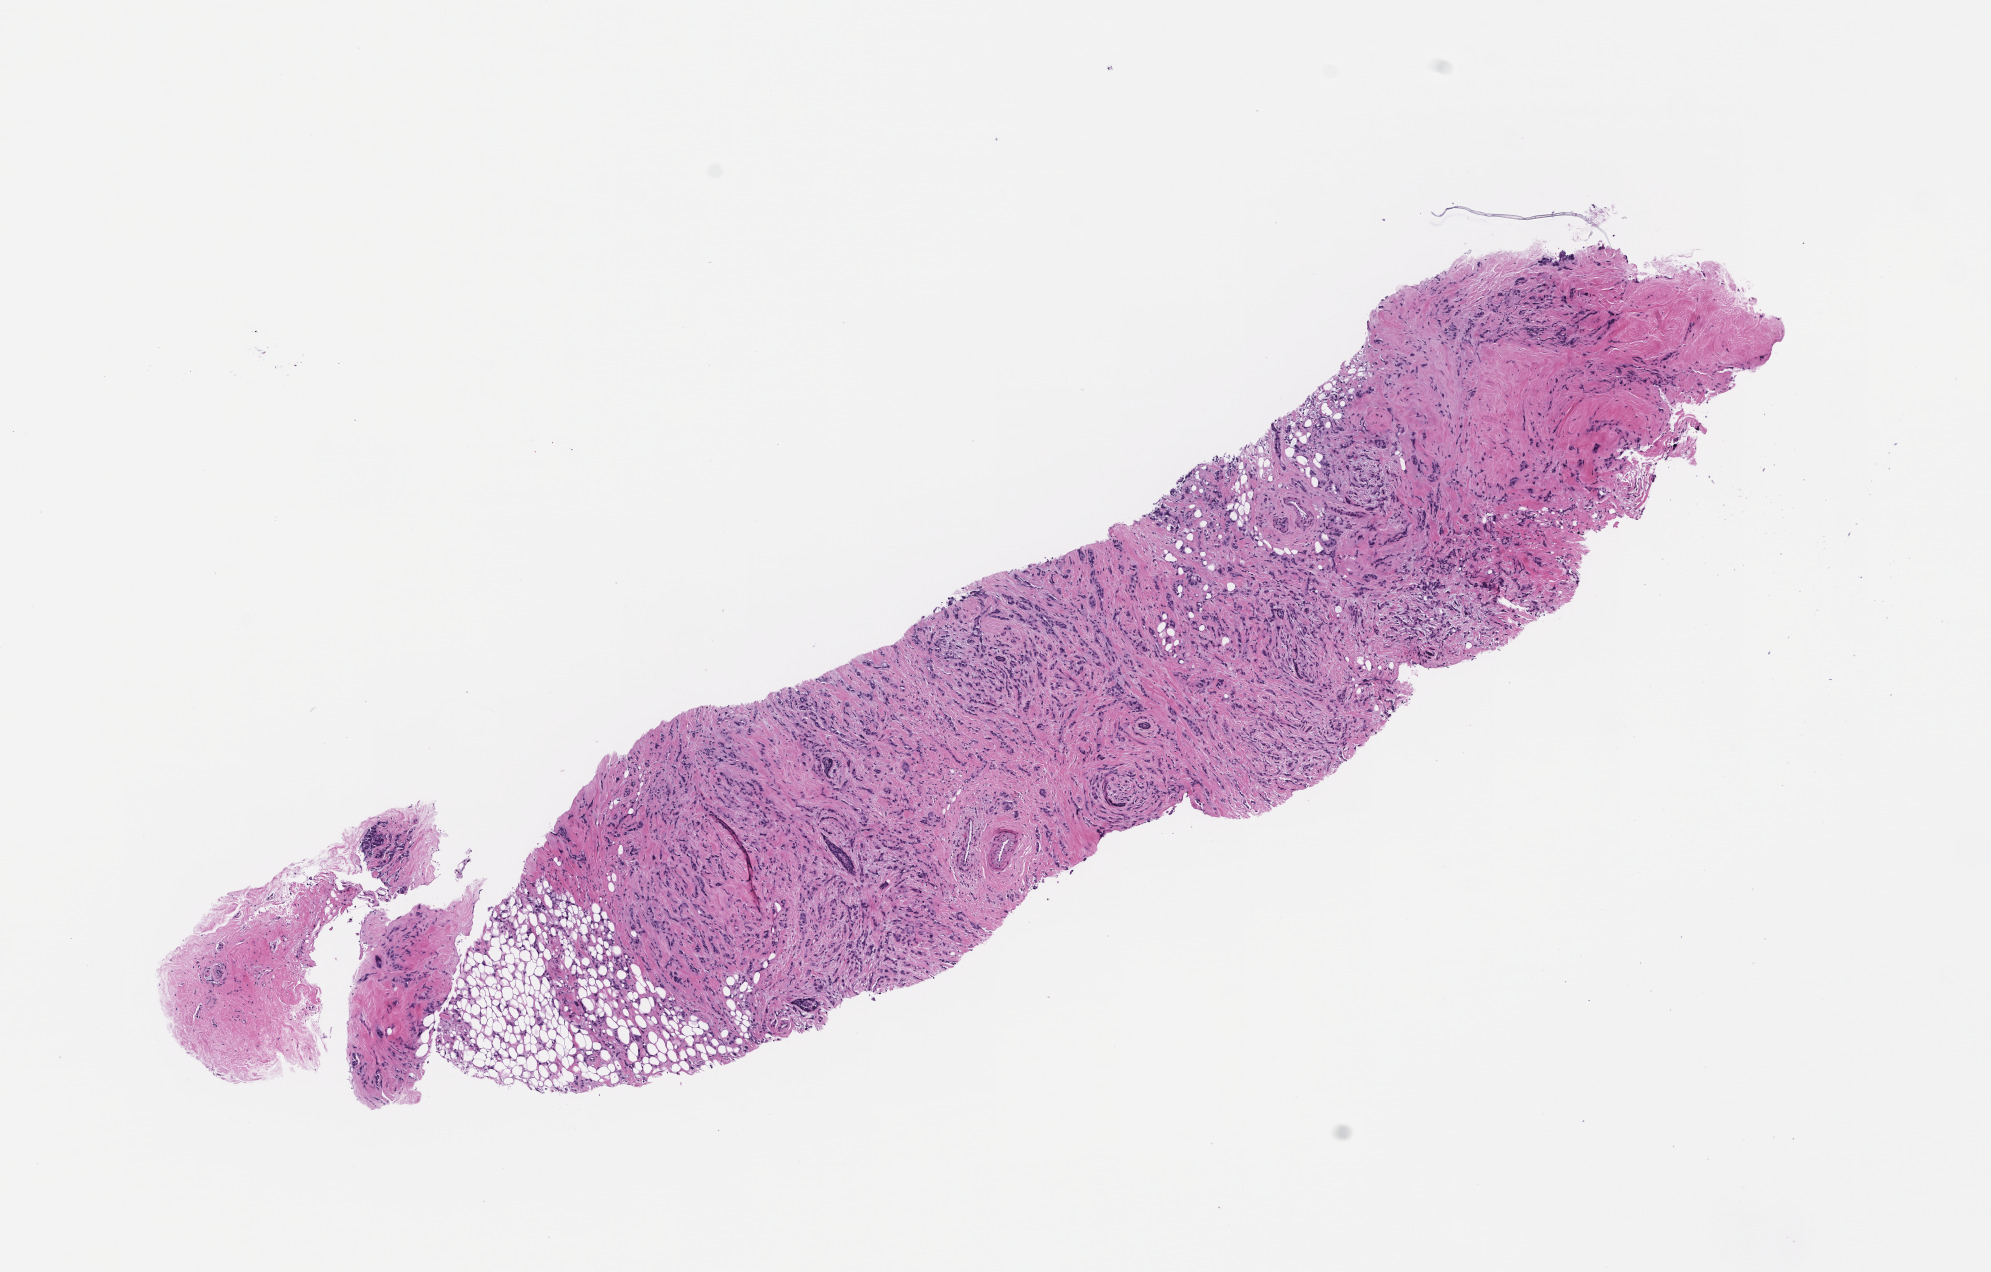
Digitized haematoxylin and eosin-stained section — a low-resolution overview of the entire scanned area, about 8.0 x 5.1 mm; formalin-fixed paraffin-embedded section; tissue site: breast. Patient sex: female.
• this section: primary tumour tissue
• diagnosis: Invasive Breast Carcinoma